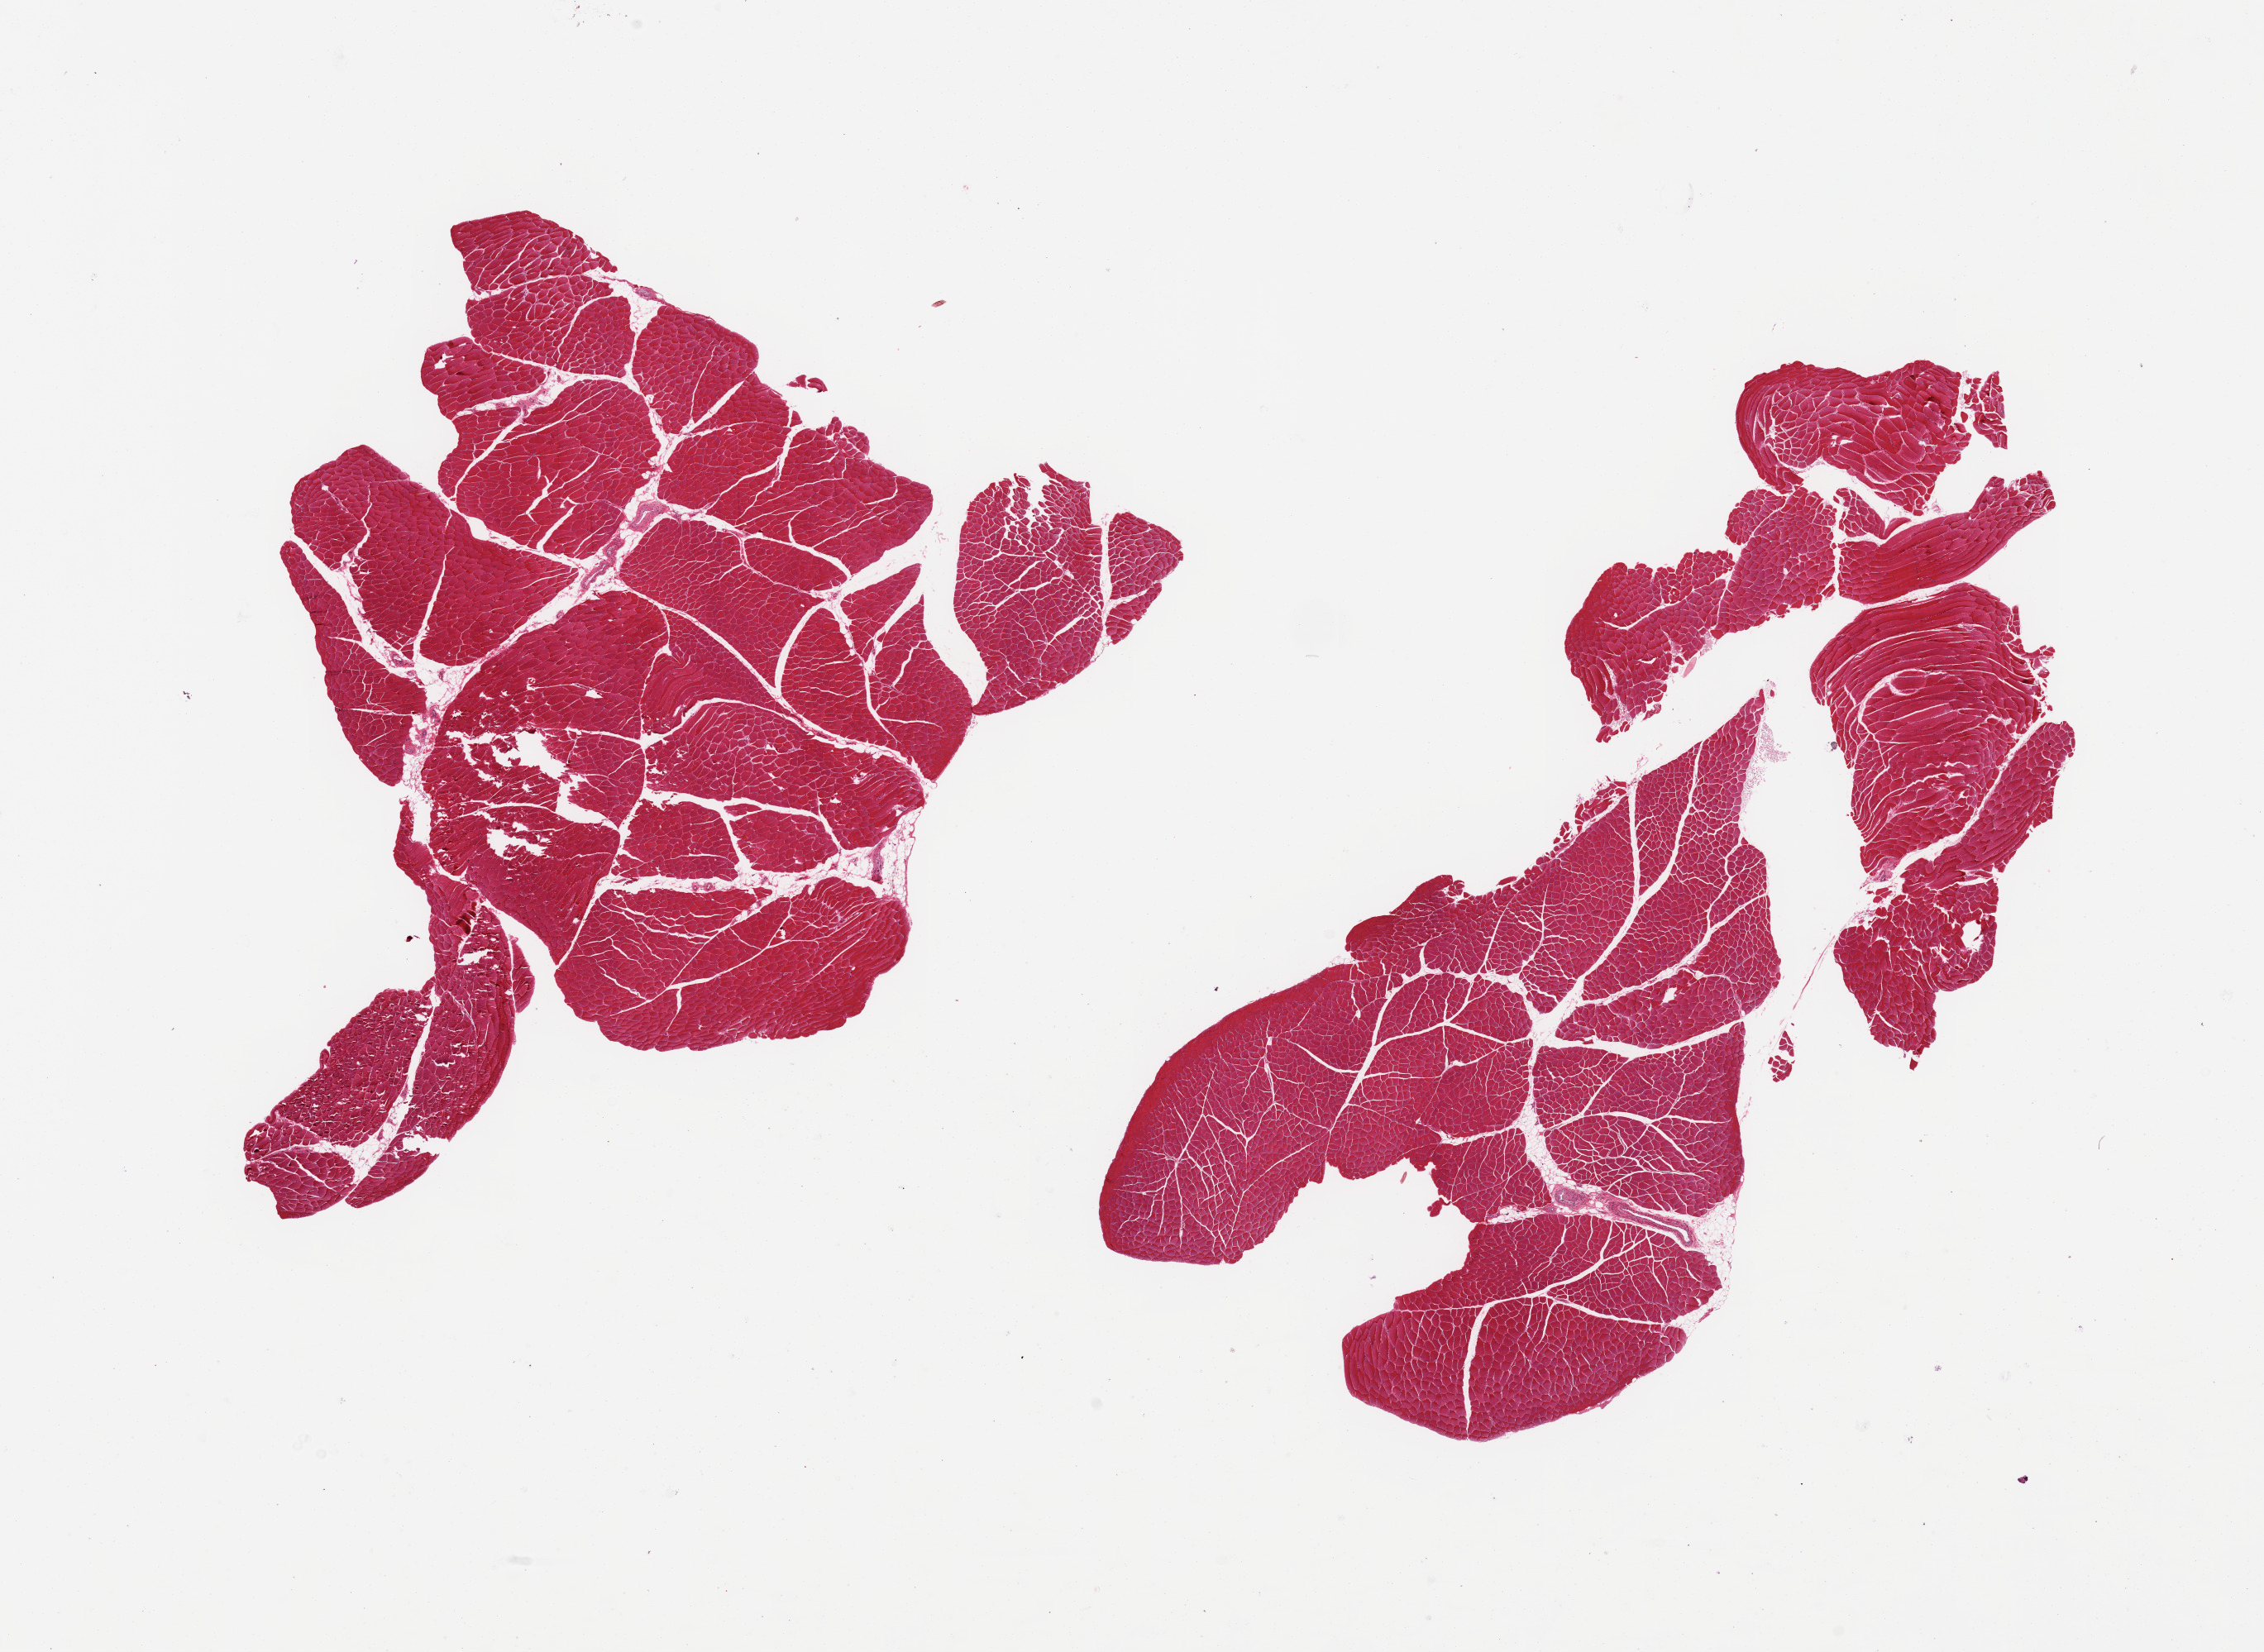
Whole-slide image, hematoxylin and eosin (H&E) stain, low-resolution overview of the scanned area, about 21.7 x 15.8 mm; PAXgene-fixed, paraffin-embedded tissue; section of skeletal muscle (target tissue); donor tissue sample.
Pathologist's review note for this sample: 2 pieces, interstitial fat/vascular elements are ~10% of tissue.